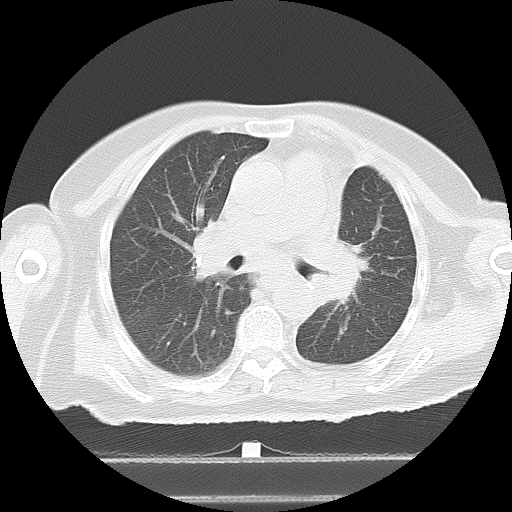
Chest CT, one axial slice. Slice 10 of 27 in the series (ordered by position). 120 kVp. Lung window (W 1500 / L -600 HU). 5 mm slice thickness. 512 × 512 image matrix, field of view 350 × 350 mm. Patient: female, 67 years. From the clinical record (not read from this slice): clinical TNM (as recorded): T1a N1 M1c.
Outlined on this slice (bounding box drawn by a radiologist):
- lung tumour (recorded histology: adenocarcinoma): bounding box [x1, y1, x2, y2] px = [334, 236, 367, 315]